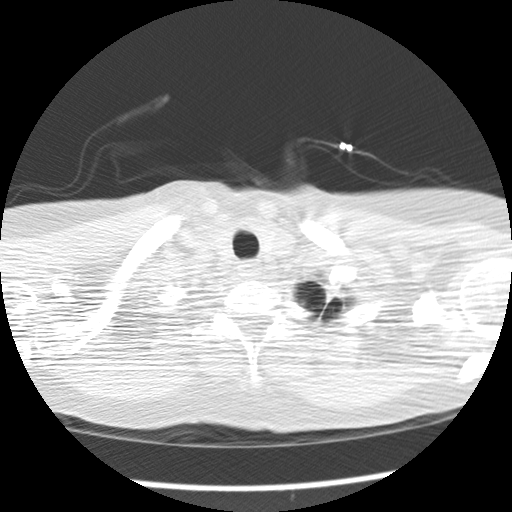
Axial slice from a low-dose chest CT screening exam, second annual screen, lung window (W 1500 / L -600 HU), standard (soft-tissue) reconstruction kernel (STANDARD), 120 kVp, 512 × 512 image matrix, field of view 308 × 308 mm. Female, age 69 years at enrolment. Former smoker at enrolment.
- Expert reader's lesion annotation, bounding box [x1, y1, x2, y2] px = [307, 274, 349, 315].
- The screening reader recorded 2 non-calcified nodules or masses ≥4 mm on this exam; which of them this box marks is not recorded.